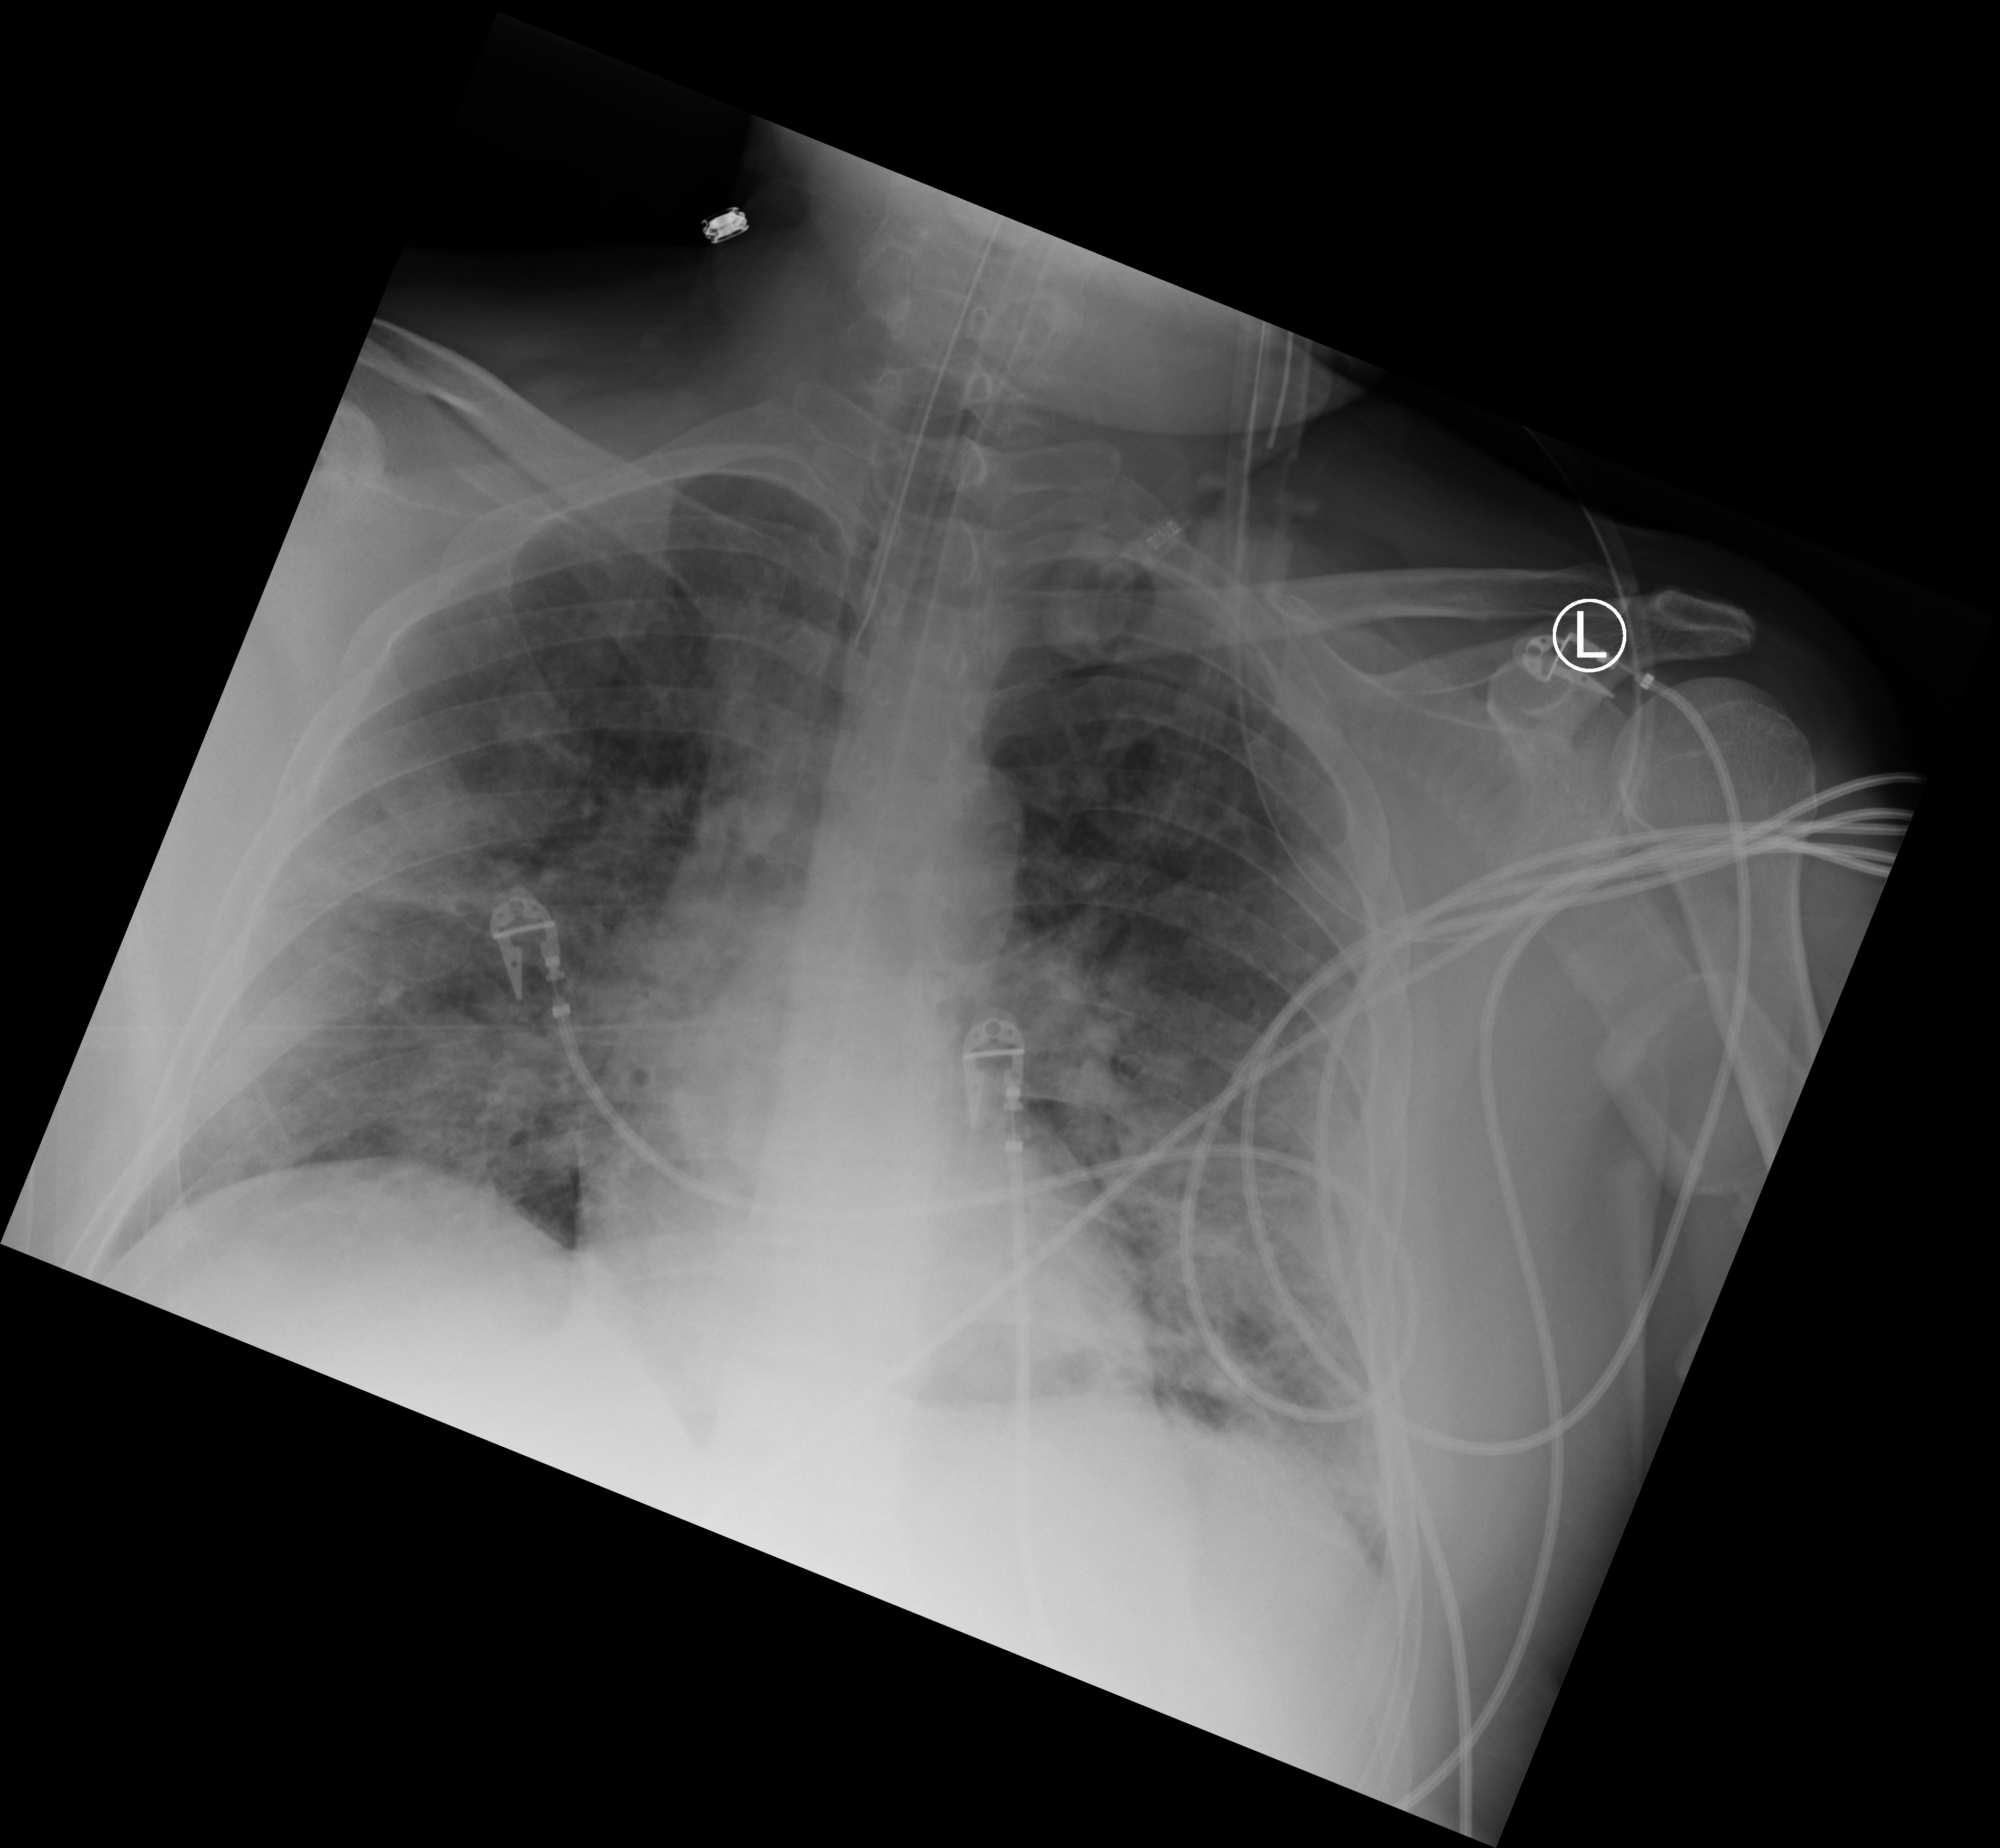
Chest X-ray (portable); anteroposterior (AP) projection. Patient hospitalised with COVID-19; male, aged 18–59 years.
Hospital-stay facts (about this admission, not read from this image; timing relative to this image not recorded): admitted to intensive care during this hospital stay: yes.